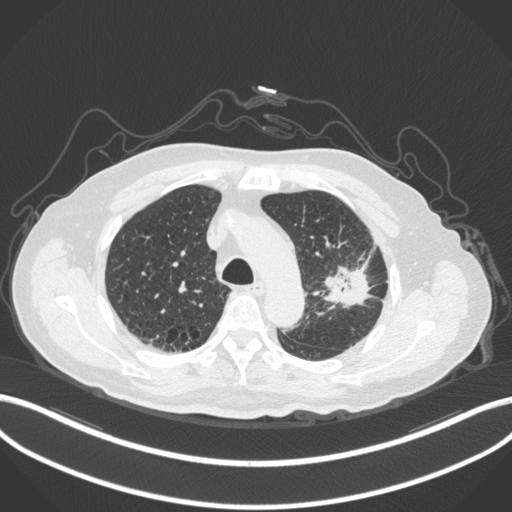
Chest CT, one axial slice; lung window (W 1500 / L -600 HU); 512 × 512 image matrix, field of view 400 × 400 mm. Male patient, age 79 years. From the clinical record (not read from this slice): clinical TNM (as recorded): T2a N1 M1.
Structures marked on this image (rectangle marked by the reading radiologist):
- lung tumour (recorded histology: adenocarcinoma): bounding box (x1, y1, x2, y2) in pixels: (319, 264, 370, 313)